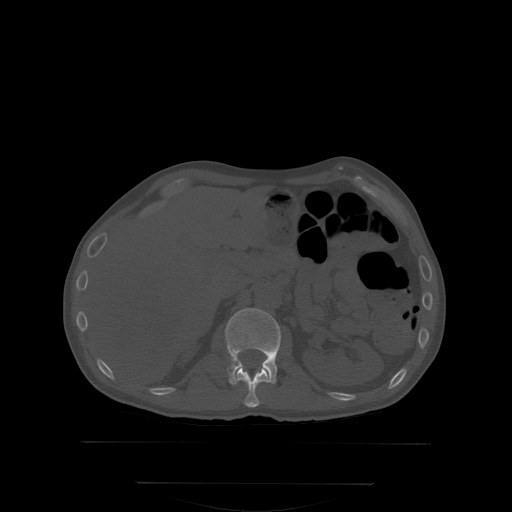
CT including the spine, one axial slice; slice 159 of 350 in the series (ordered by position); bone window (W 1800 / L 400 HU); 2.5 mm slice thickness; 512 × 512 image matrix, field of view 500 × 500 mm. Patient: male, 58 years. Case-level facts recorded for this patient, not image findings: primary cancer: prostate.
Structures marked on this image (semi-automatic segmentation, software-assisted and operator-edited):
- L1 vertebra: bounding box (x1, y1, x2, y2) in pixels: (225, 308, 280, 384)
- T12 vertebra: (237, 365, 270, 407)